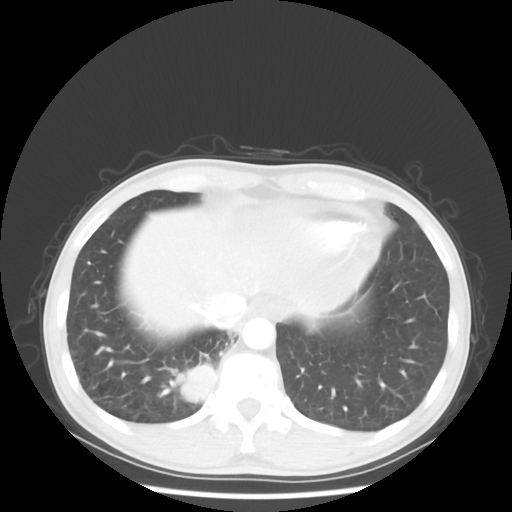
Chest CT, one axial slice. Slice 9 of 58 in the series (ordered by position). Reconstruction kernel STANDARD. 100 kVp. Lung window (W 1500 / L -600 HU). 512 × 512 image matrix. Patient: male, 56 years. From the clinical record (not read from this slice): clinical TNM (as recorded): T2 N1 M1; histopathological grade: G1.
Outlined on this slice (rectangle marked by the reading radiologist):
- lung tumour (recorded histology: adenocarcinoma): bounding box <175,361,220,404> (left, top, right, bottom; pixels)